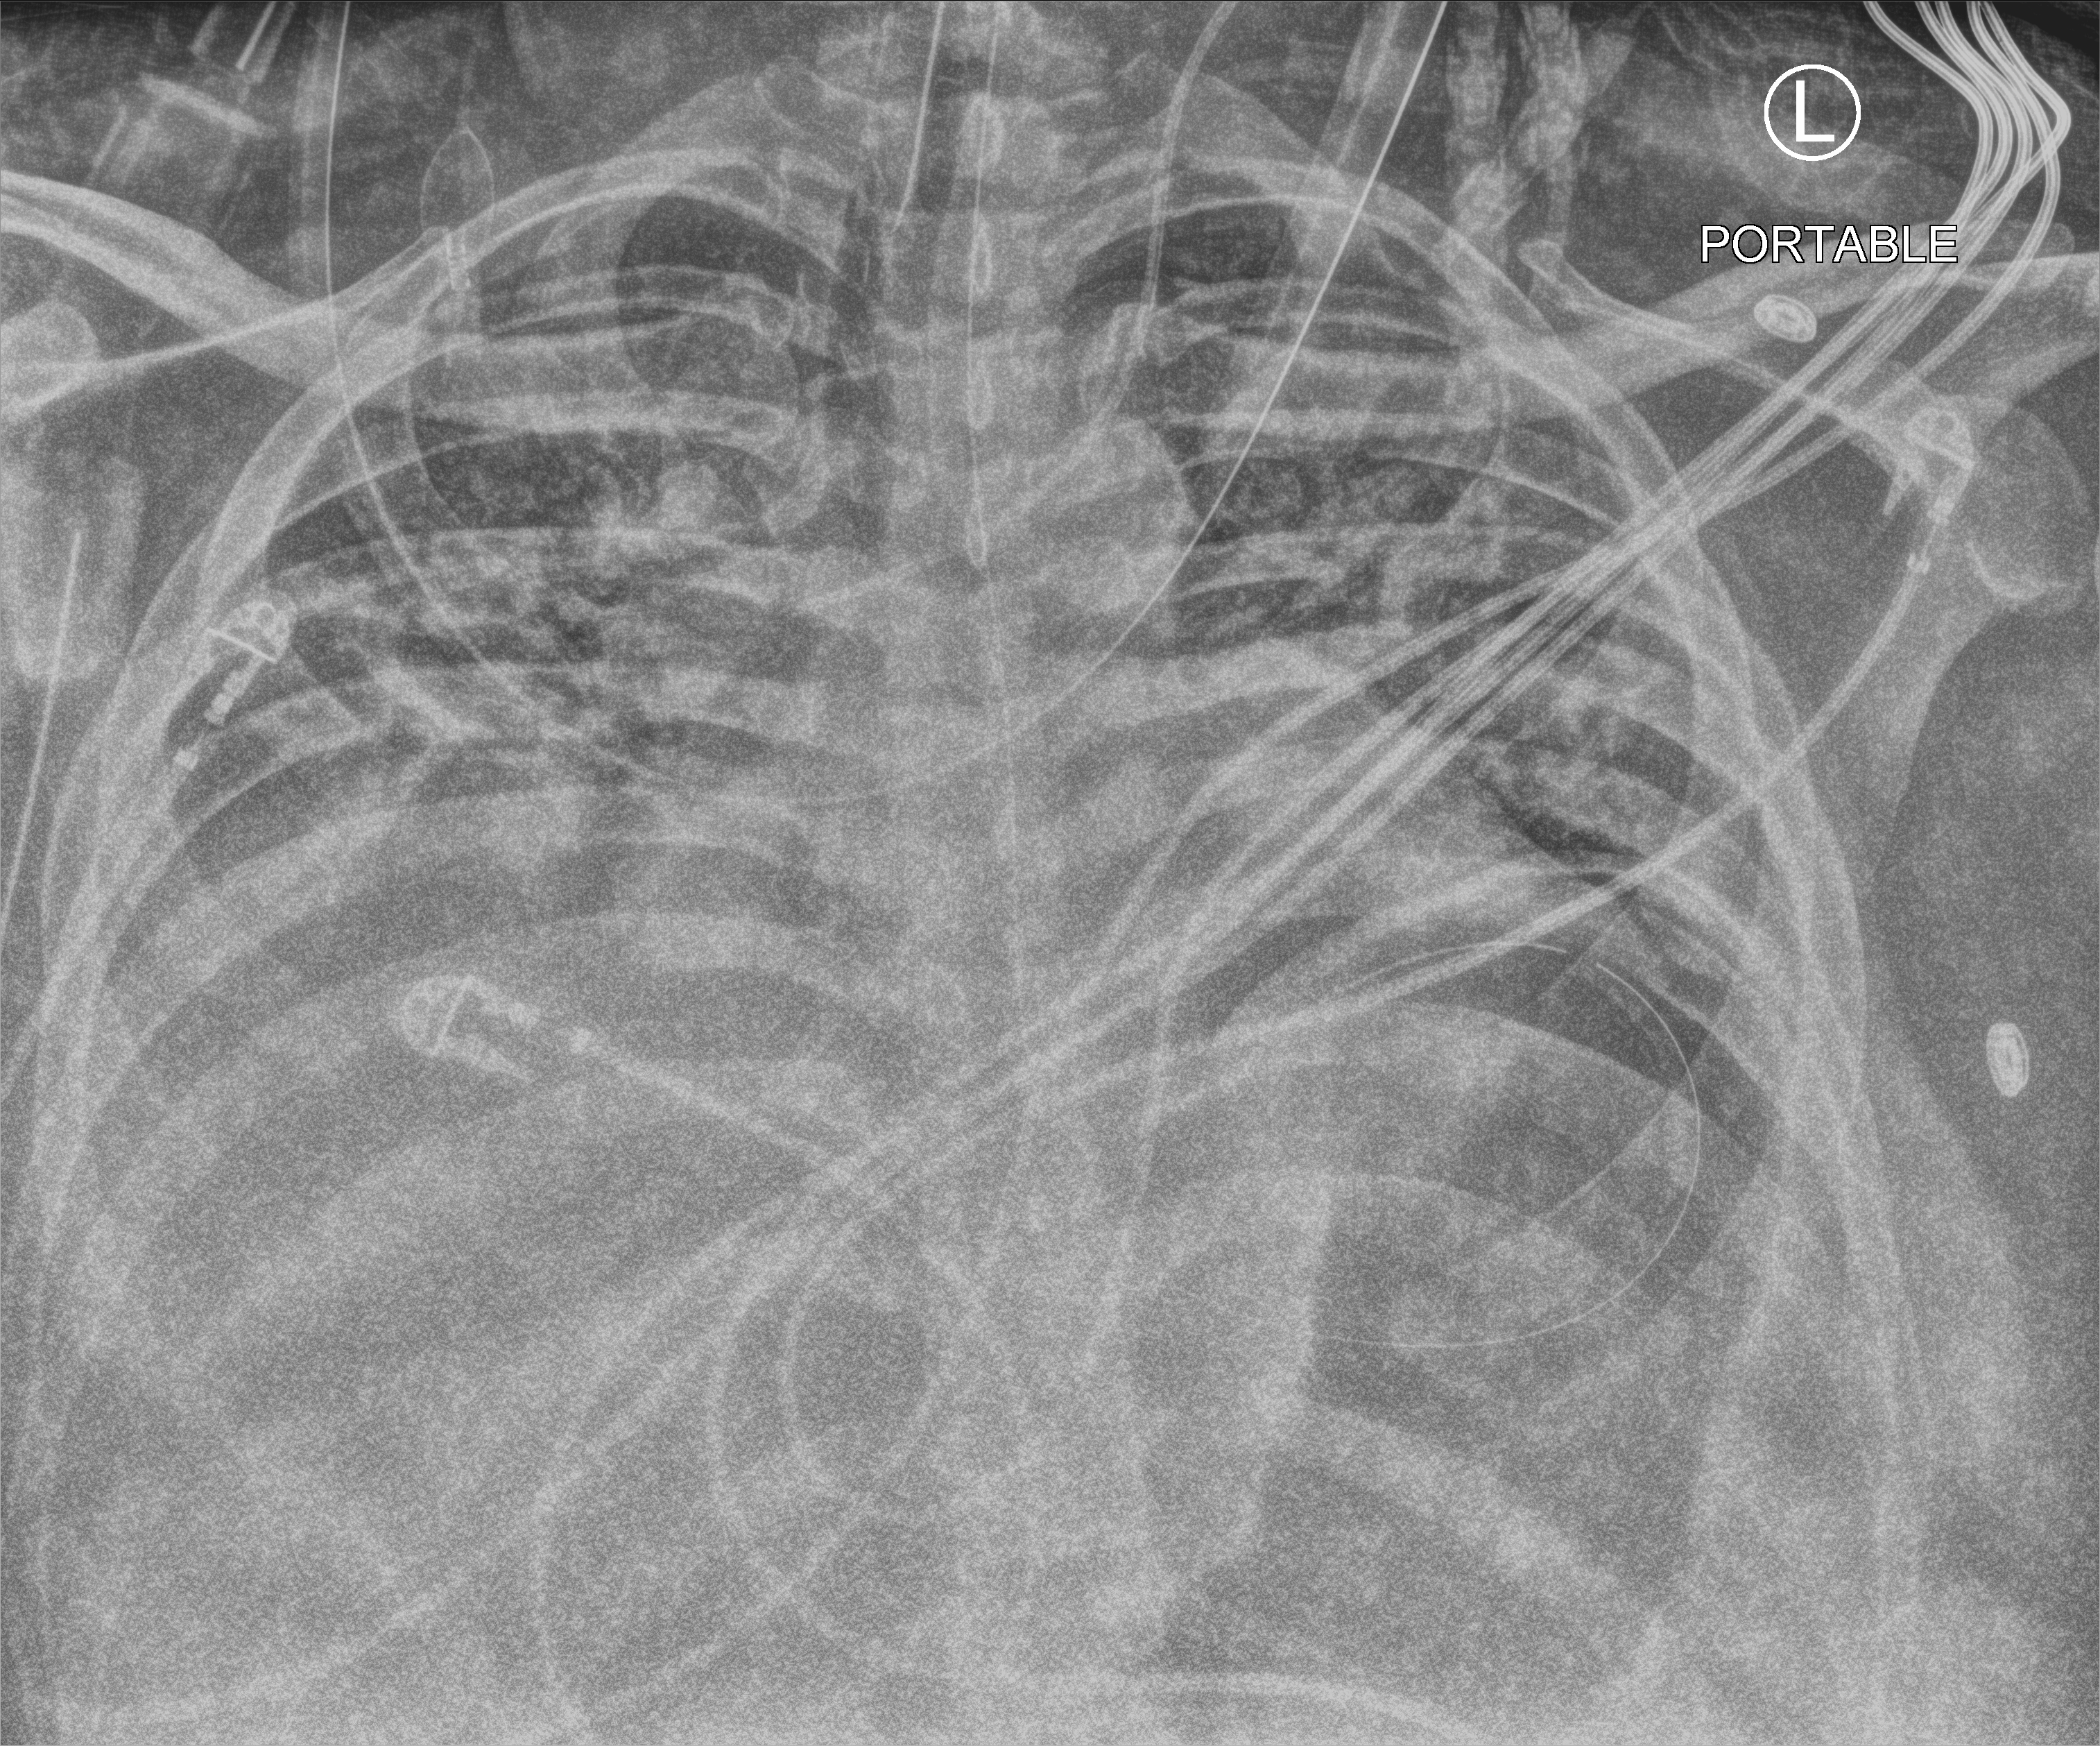
Chest X-ray (portable). Patient hospitalised with COVID-19; male, aged 18–59 years.
Hospital-stay facts (about this admission, not read from this image; timing relative to this image not recorded): mechanically ventilated during this hospital stay: yes; admitted to intensive care during this hospital stay: yes.